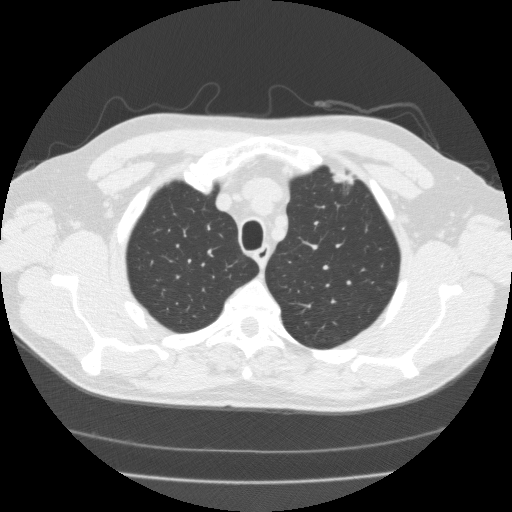
Axial slice from a low-dose chest CT screening exam; third annual screen; lung window (W 1500 / L -600 HU); 512 × 512 image matrix, field of view 359 × 359 mm. Male, age 56 years at enrolment. Former smoker at enrolment.
Expert reader's lesion annotation, bounding box [x1, y1, x2, y2] px = [323, 158, 366, 194]. The exam's reader record, not a measurement of the box and not confirmed to be the same lesion: non-calcified nodule or mass ≥4 mm, left upper lobe, 18 × 10 mm, spiculated (stellate) margins, soft tissue attenuation, pre-existing on the prior screen: yes; interval growth: yes. Official screen result: positive, other. Participant outcome: lung cancer diagnosed 119 days after this screen — adenocarcinoma, NOS, left upper lobe, moderately differentiated (G2), stage IA (AJCC 6th edition), 15 mm at pathology.